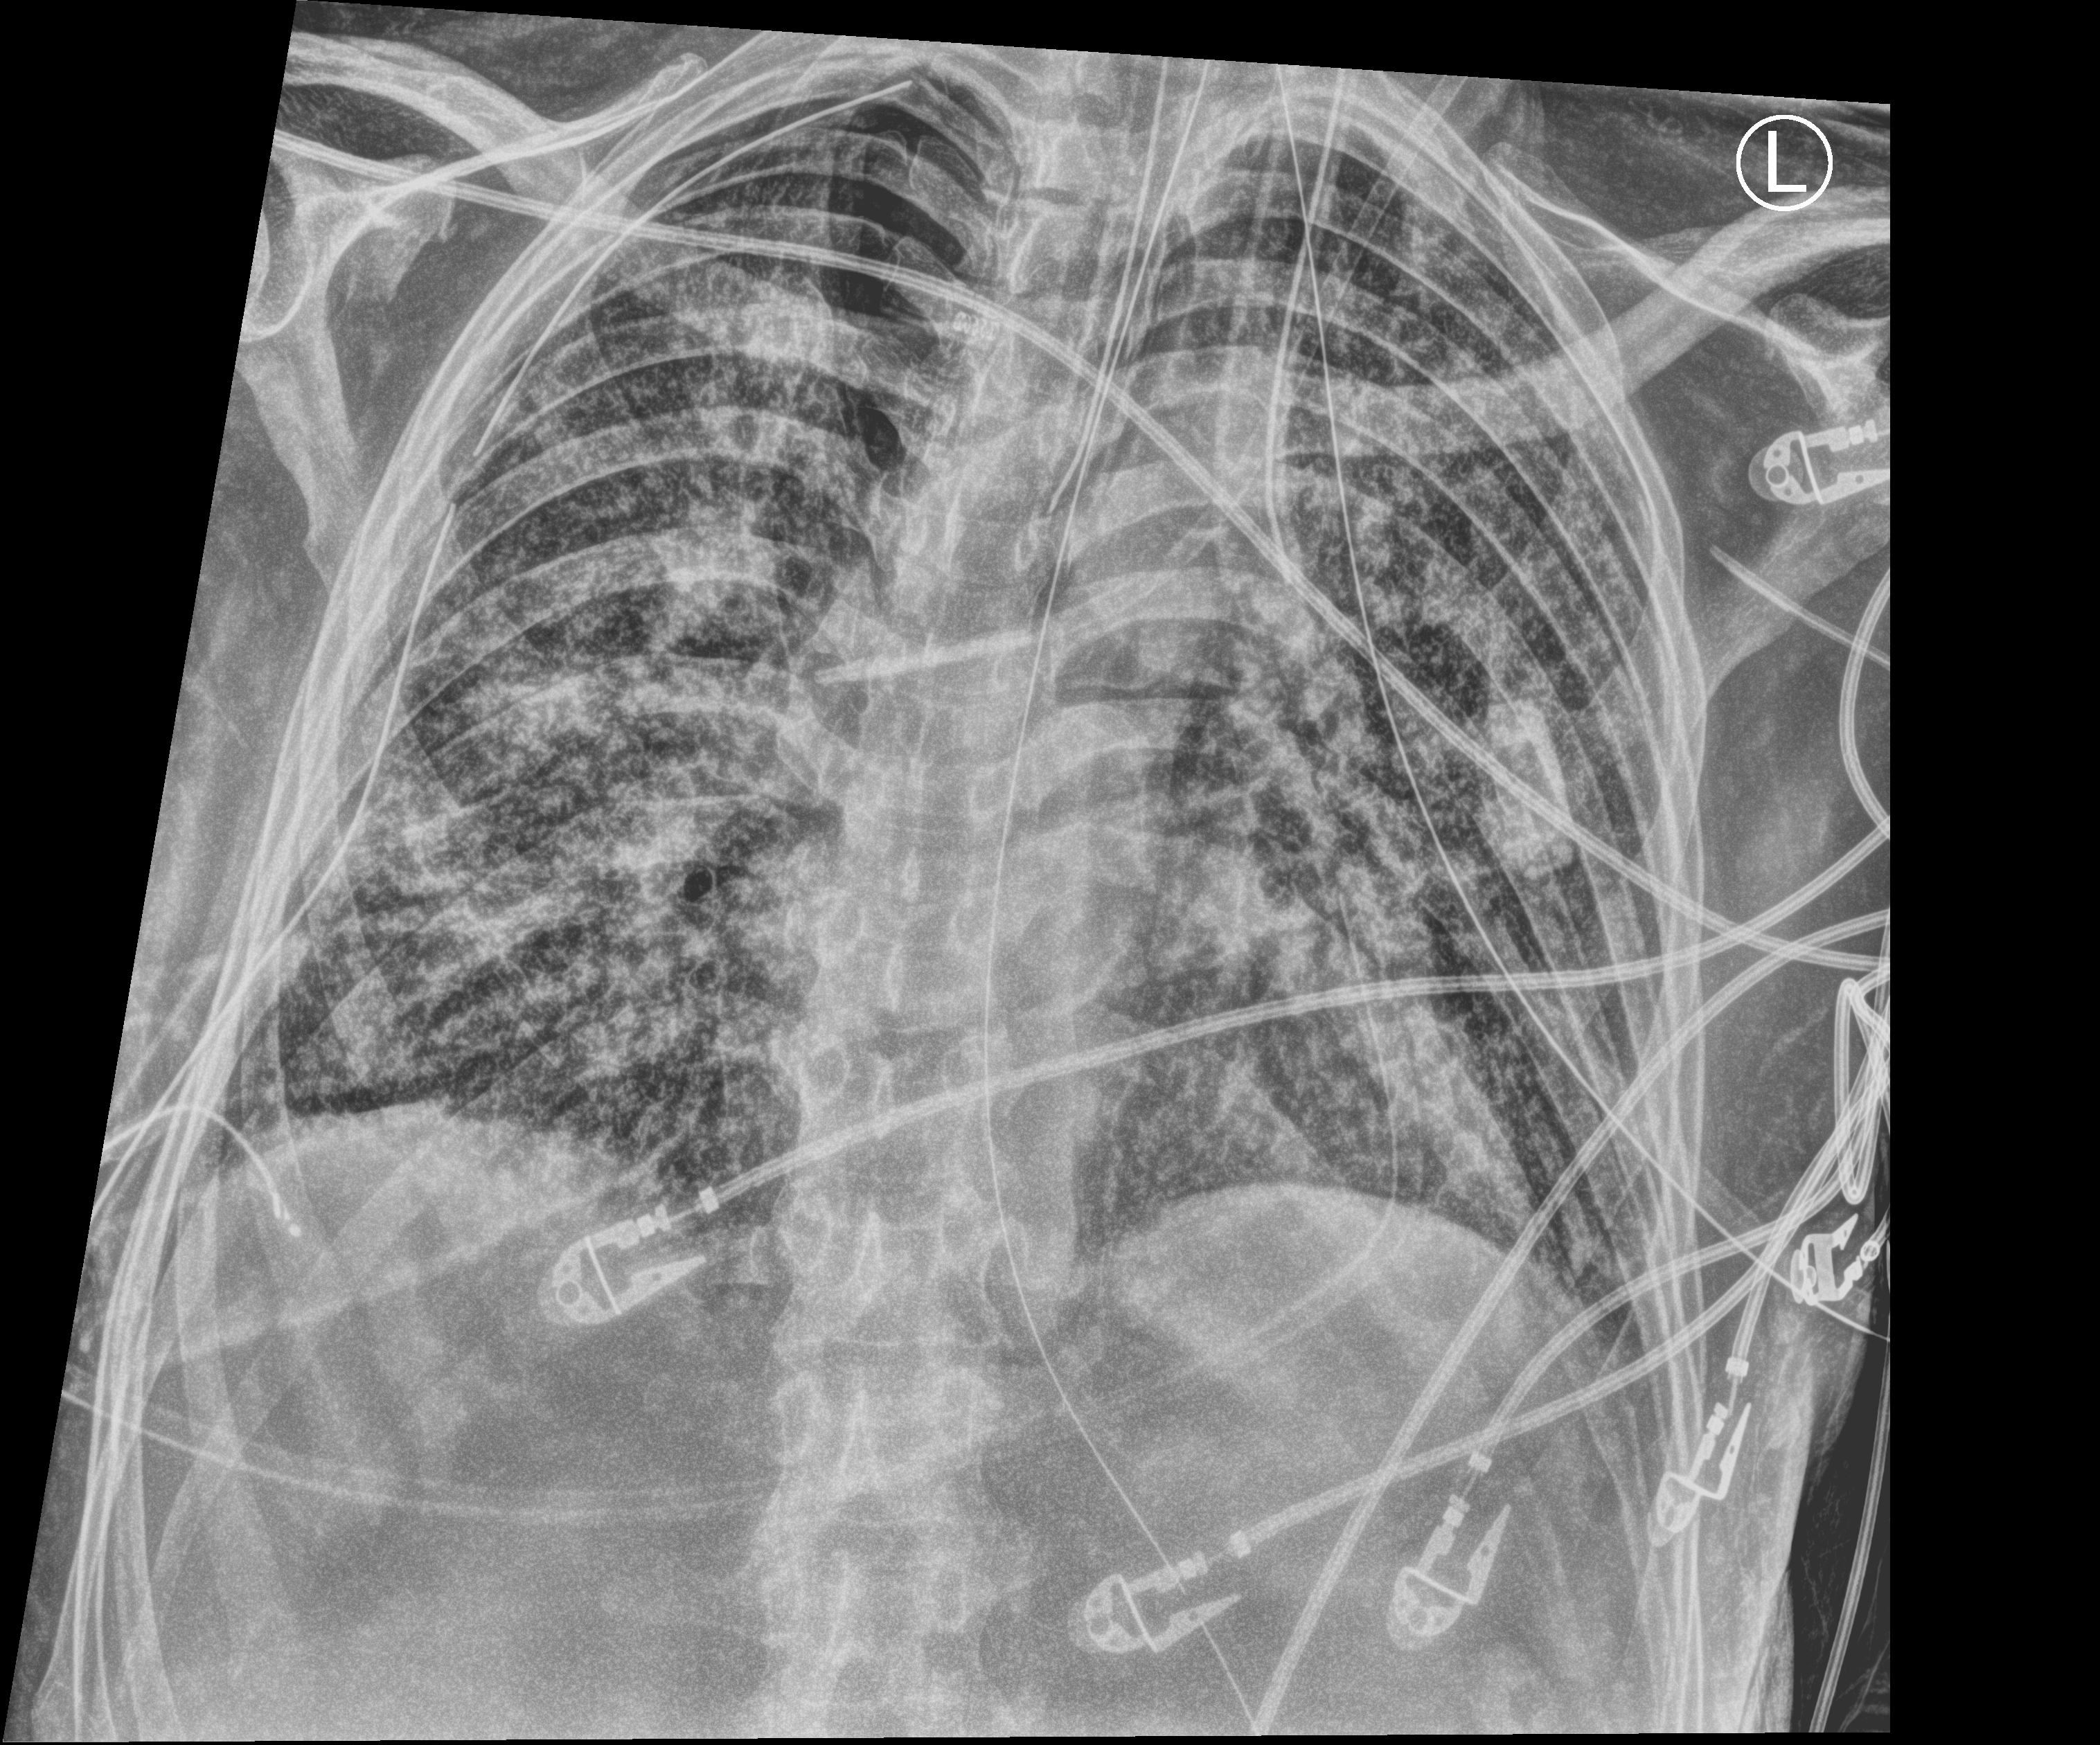
Bedside chest radiograph (computed radiography), anteroposterior (AP) projection. Patient hospitalised with COVID-19; male, aged 60–74 years.
Admission-level facts for this patient (not findings on this image; timing relative to this image not recorded): smoking status (admission record): never; admitted to intensive care during this hospital stay: yes; mechanically ventilated during this hospital stay: yes.